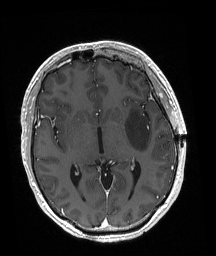
Brain MRI from a brain-tumour surgery series, one axial slice. Slice 104 of 192 in the series (ordered by position). T1-weighted post-contrast. 1 mm slice thickness. 216 × 256 image matrix, field of view 211 × 250 mm. From the clinical record (not read from this slice): histopathology: Astrocytoma; WHO grade: 3; IDH mutation: yes.
Outlined on this slice (expert manual segmentation):
- tumour: bounding box <126,109,152,152> (left, top, right, bottom; pixels)